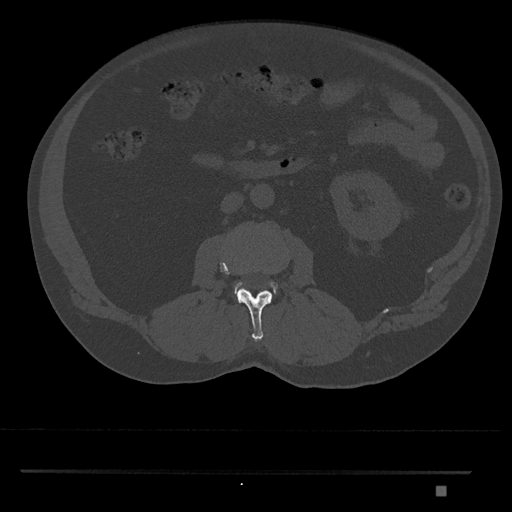
CT including the spine, one axial slice. Slice 727 of 1134 in the series (ordered by position). 120 kVp. Bone window (W 1800 / L 400 HU). 512 × 512 image matrix, field of view 429 × 429 mm. Male patient, age 65 years. Case-level facts recorded for this patient, not image findings: primary cancer: prostate.
Outlined on this slice (semi-automatic segmentation, software-assisted and operator-edited):
- L2 vertebra: bounding box [x1, y1, x2, y2] px = [220, 260, 272, 342]
- L3 vertebra: [234, 281, 278, 293]